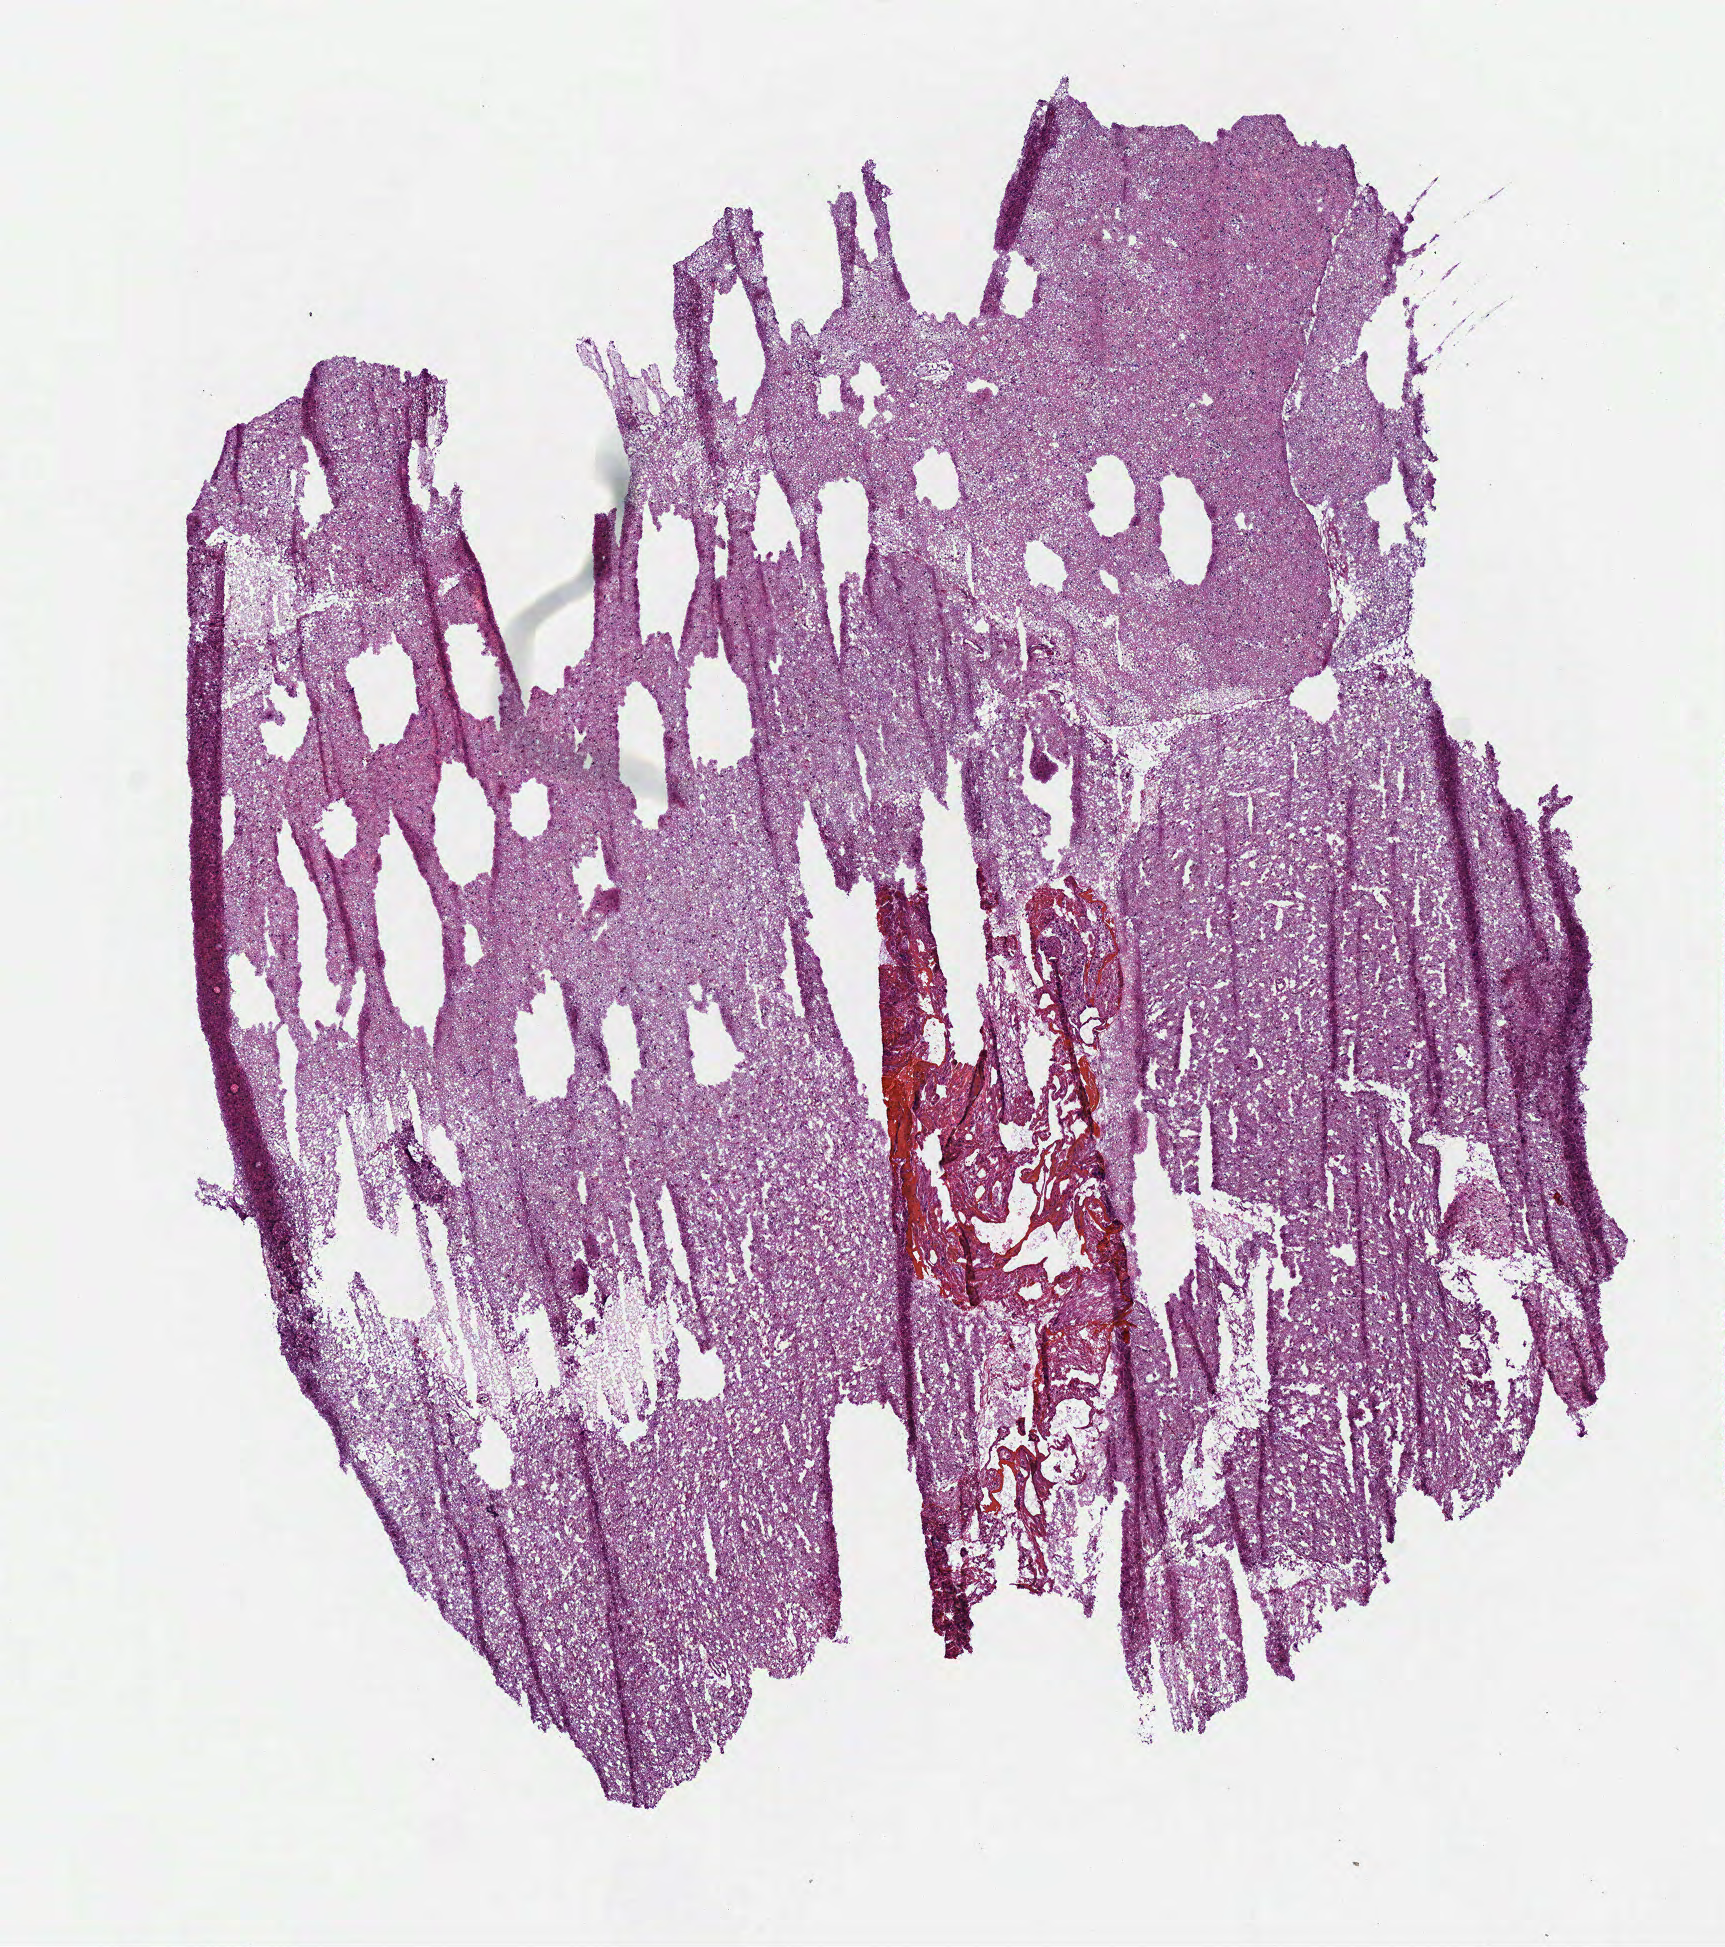
Digitized Hematoxylin and eosin (H&E) stained tissue section (whole slide), whole scanned area (about 6.8 x 7.7 mm, slide scanned at 40x) shown as a low-resolution overview. Frozen section. Sample: primary tumour, brain. Female, age 57 years at initial diagnosis. Histologic grade: G3 (poorly differentiated). Pathologist review of this section (percent, as recorded): tumour cells 100%, tumour nuclei 65%, normal cells 0%, stromal cells 0%, necrosis 0%.
Laterality: right. Histologic diagnosis: Astrocytoma, anaplastic.